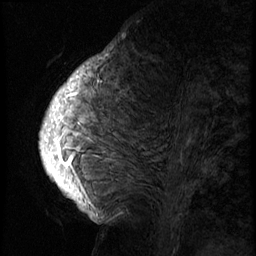
Breast MRI (dynamic contrast-enhanced), one sagittal slice; position 28 of 74 along the scan axis; 3 images stored at this slice position (order not interpretable as contrast timing); 1.5 T; TE 4.2 ms, TR 8.9 ms; 2.5 mm slice thickness; 256 × 256 image matrix, field of view 200 × 200 mm. Female patient, age 57 years. Case-level facts recorded for this patient, not image findings: setting: breast cancer imaged before/during neoadjuvant chemotherapy; receptor status: HER2-positive.
Outlined on this slice (semi-automatically segmented with operator editing):
- analysis volume of interest (the breast-tissue region the enhancement analysis was run in; not a lesion): box from (x=40, y=62) to (x=239, y=175) px
- tumour enhancement mask (voxels above the 140 % enhancement threshold inside the analysis volume of interest): (x=50, y=63)–(x=101, y=175)